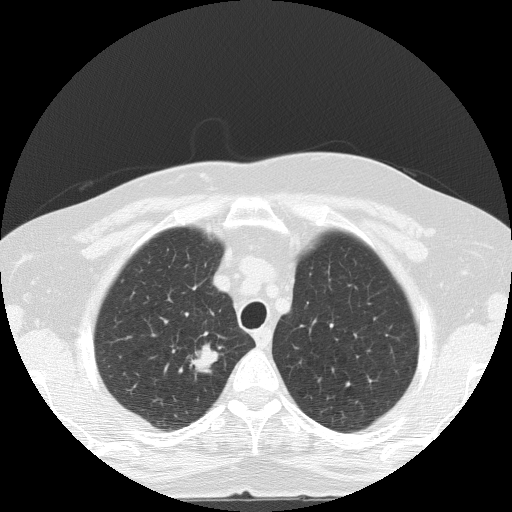
Chest CT (low-dose screening protocol), one axial image. Baseline screening round. Lung window (W 1500 / L -600 HU). Slice 24 of 133 in the series. Female participant, aged 56 years at enrolment. Current smoker at enrolment.
- Lesion marked by an expert reader, bounding box <170,337,235,389> (left, top, right, bottom; pixels).
- The screening reader recorded 2 non-calcified nodules or masses ≥4 mm on this exam (right upper lobe, right lower lobe); which of them this box marks is not recorded.